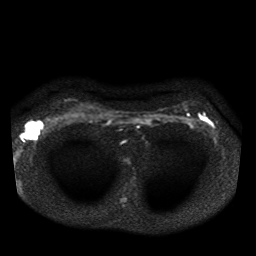
Breast MRI, one axial slice. Slice 30 of 41 in the series (ordered by position). Diffusion-weighted series; image 2 of 4 stored at this slice position (different b-values; order by instance number). 1.5 T. 5 mm slice thickness. 256 × 256 image matrix, field of view 330 × 330 mm. Female patient.
Outlined on this slice (expert manual segmentation):
- tumour on diffusion-weighted imaging: box from (x=25, y=122) to (x=37, y=139) px